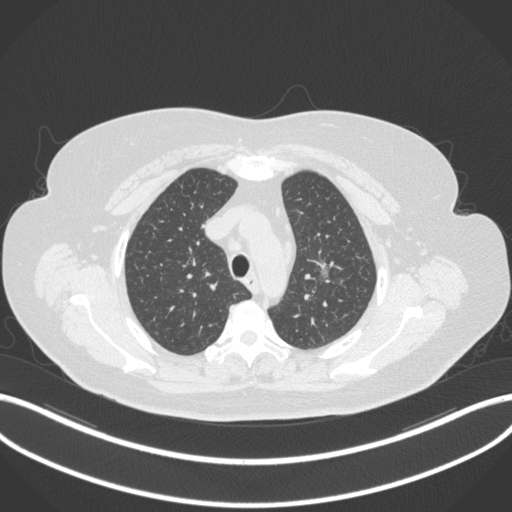
Chest CT, one axial slice. Reconstruction kernel B31f. 120 kVp. Lung window (W 1500 / L -600 HU). 1 mm slice thickness. 512 × 512 image matrix, field of view 400 × 400 mm. Female patient, age 70 years. From the clinical record (not read from this slice): clinical TNM (as recorded): T1c N0 M0.
Outlined on this slice (bounding box drawn by a radiologist):
- lung tumour (recorded histology: adenocarcinoma): bounding box <312,251,343,287> (left, top, right, bottom; pixels)